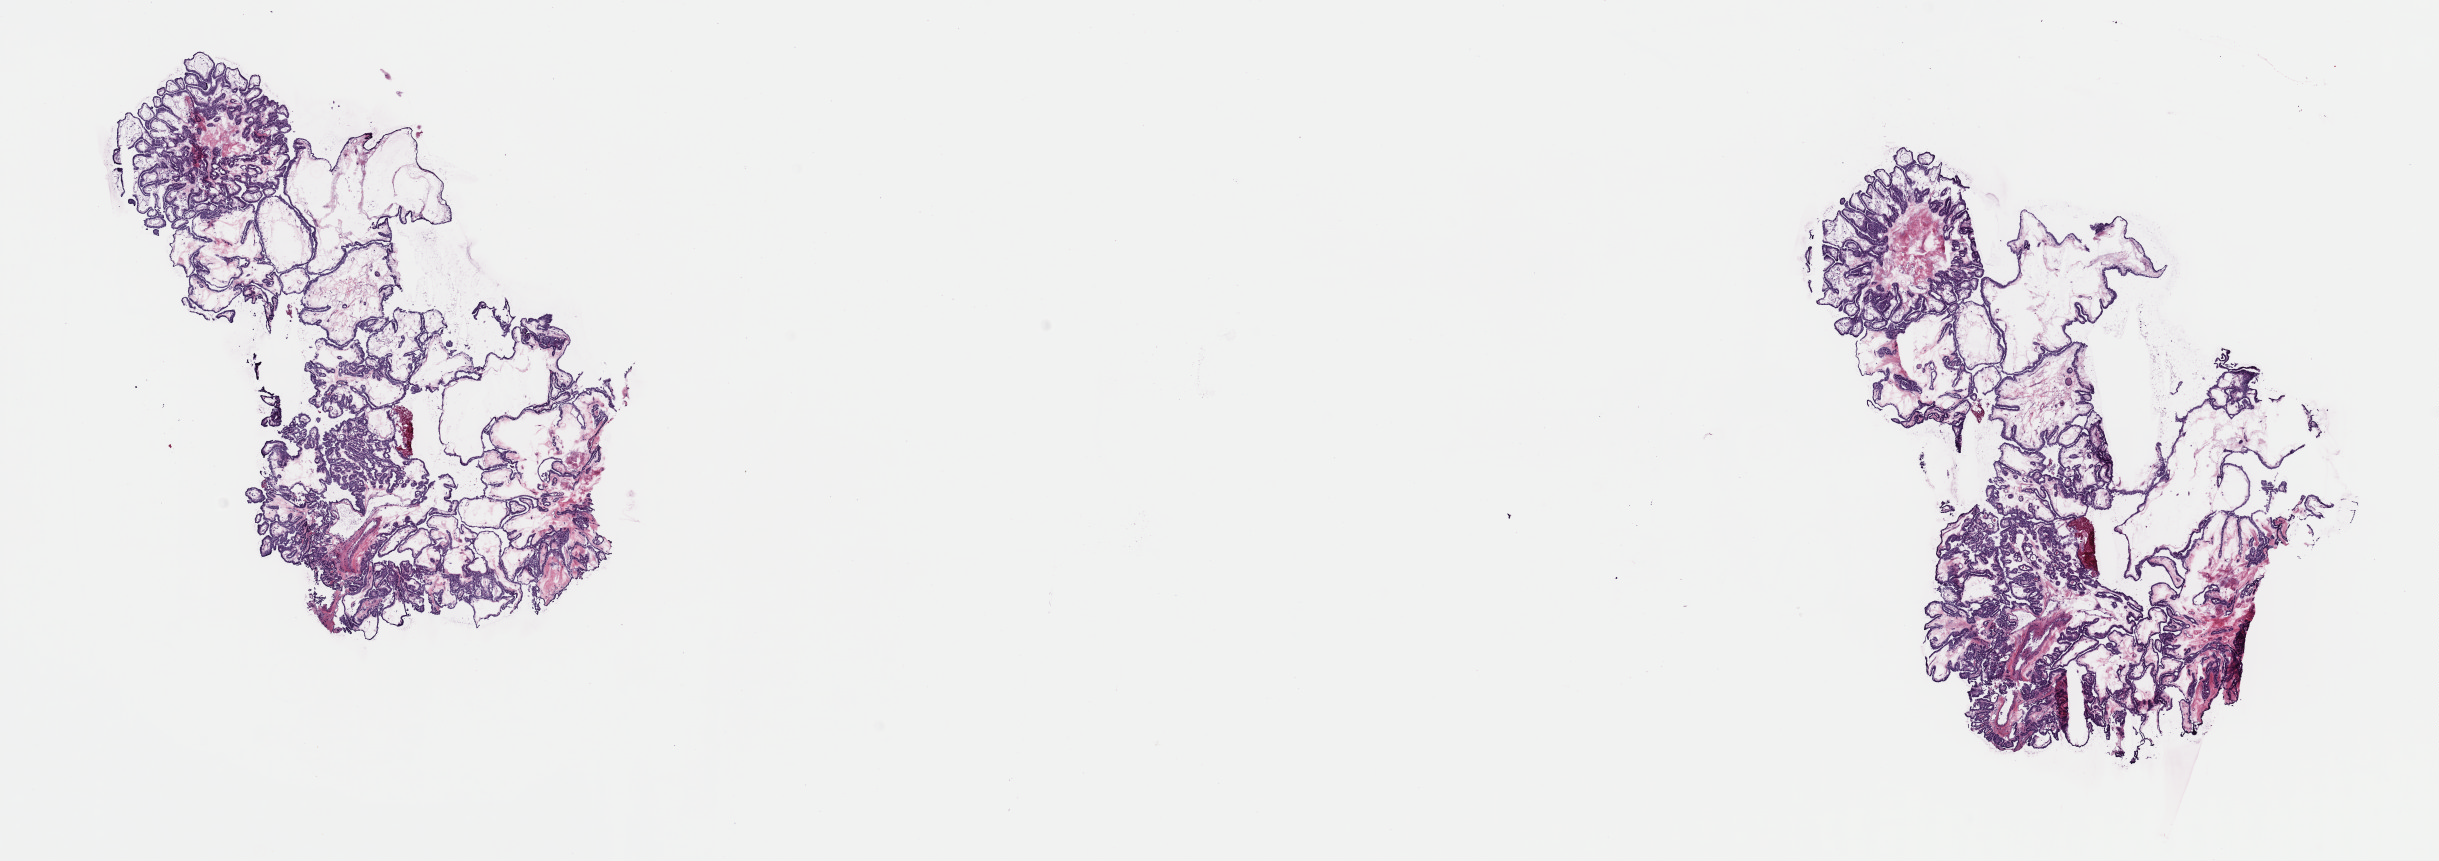
Hematoxylin and eosin (H&E) stained whole-slide image — whole scanned area (about 19.3 x 6.8 mm, slide scanned at 40x) shown as a low-resolution overview; frozen section from the top of the tissue portion; thyroid, primary tumour sample. Patient: female, age at initial diagnosis 40 years. Pathologist review of this section (percent, as recorded): tumour cells 100%, tumour nuclei 85%, normal cells 0%, stromal cells 0%, necrosis 0%. Inflammatory infiltration, as recorded: lymphocyte infiltration 2%, monocyte infiltration 0%, neutrophil infiltration 0%.
• diagnosis: Papillary adenocarcinoma, NOS (thyroid gland)
• laterality: right
• AJCC pathologic stage: I (7th edition)
• lymph nodes positive (case pathology): 0 of 3 examined